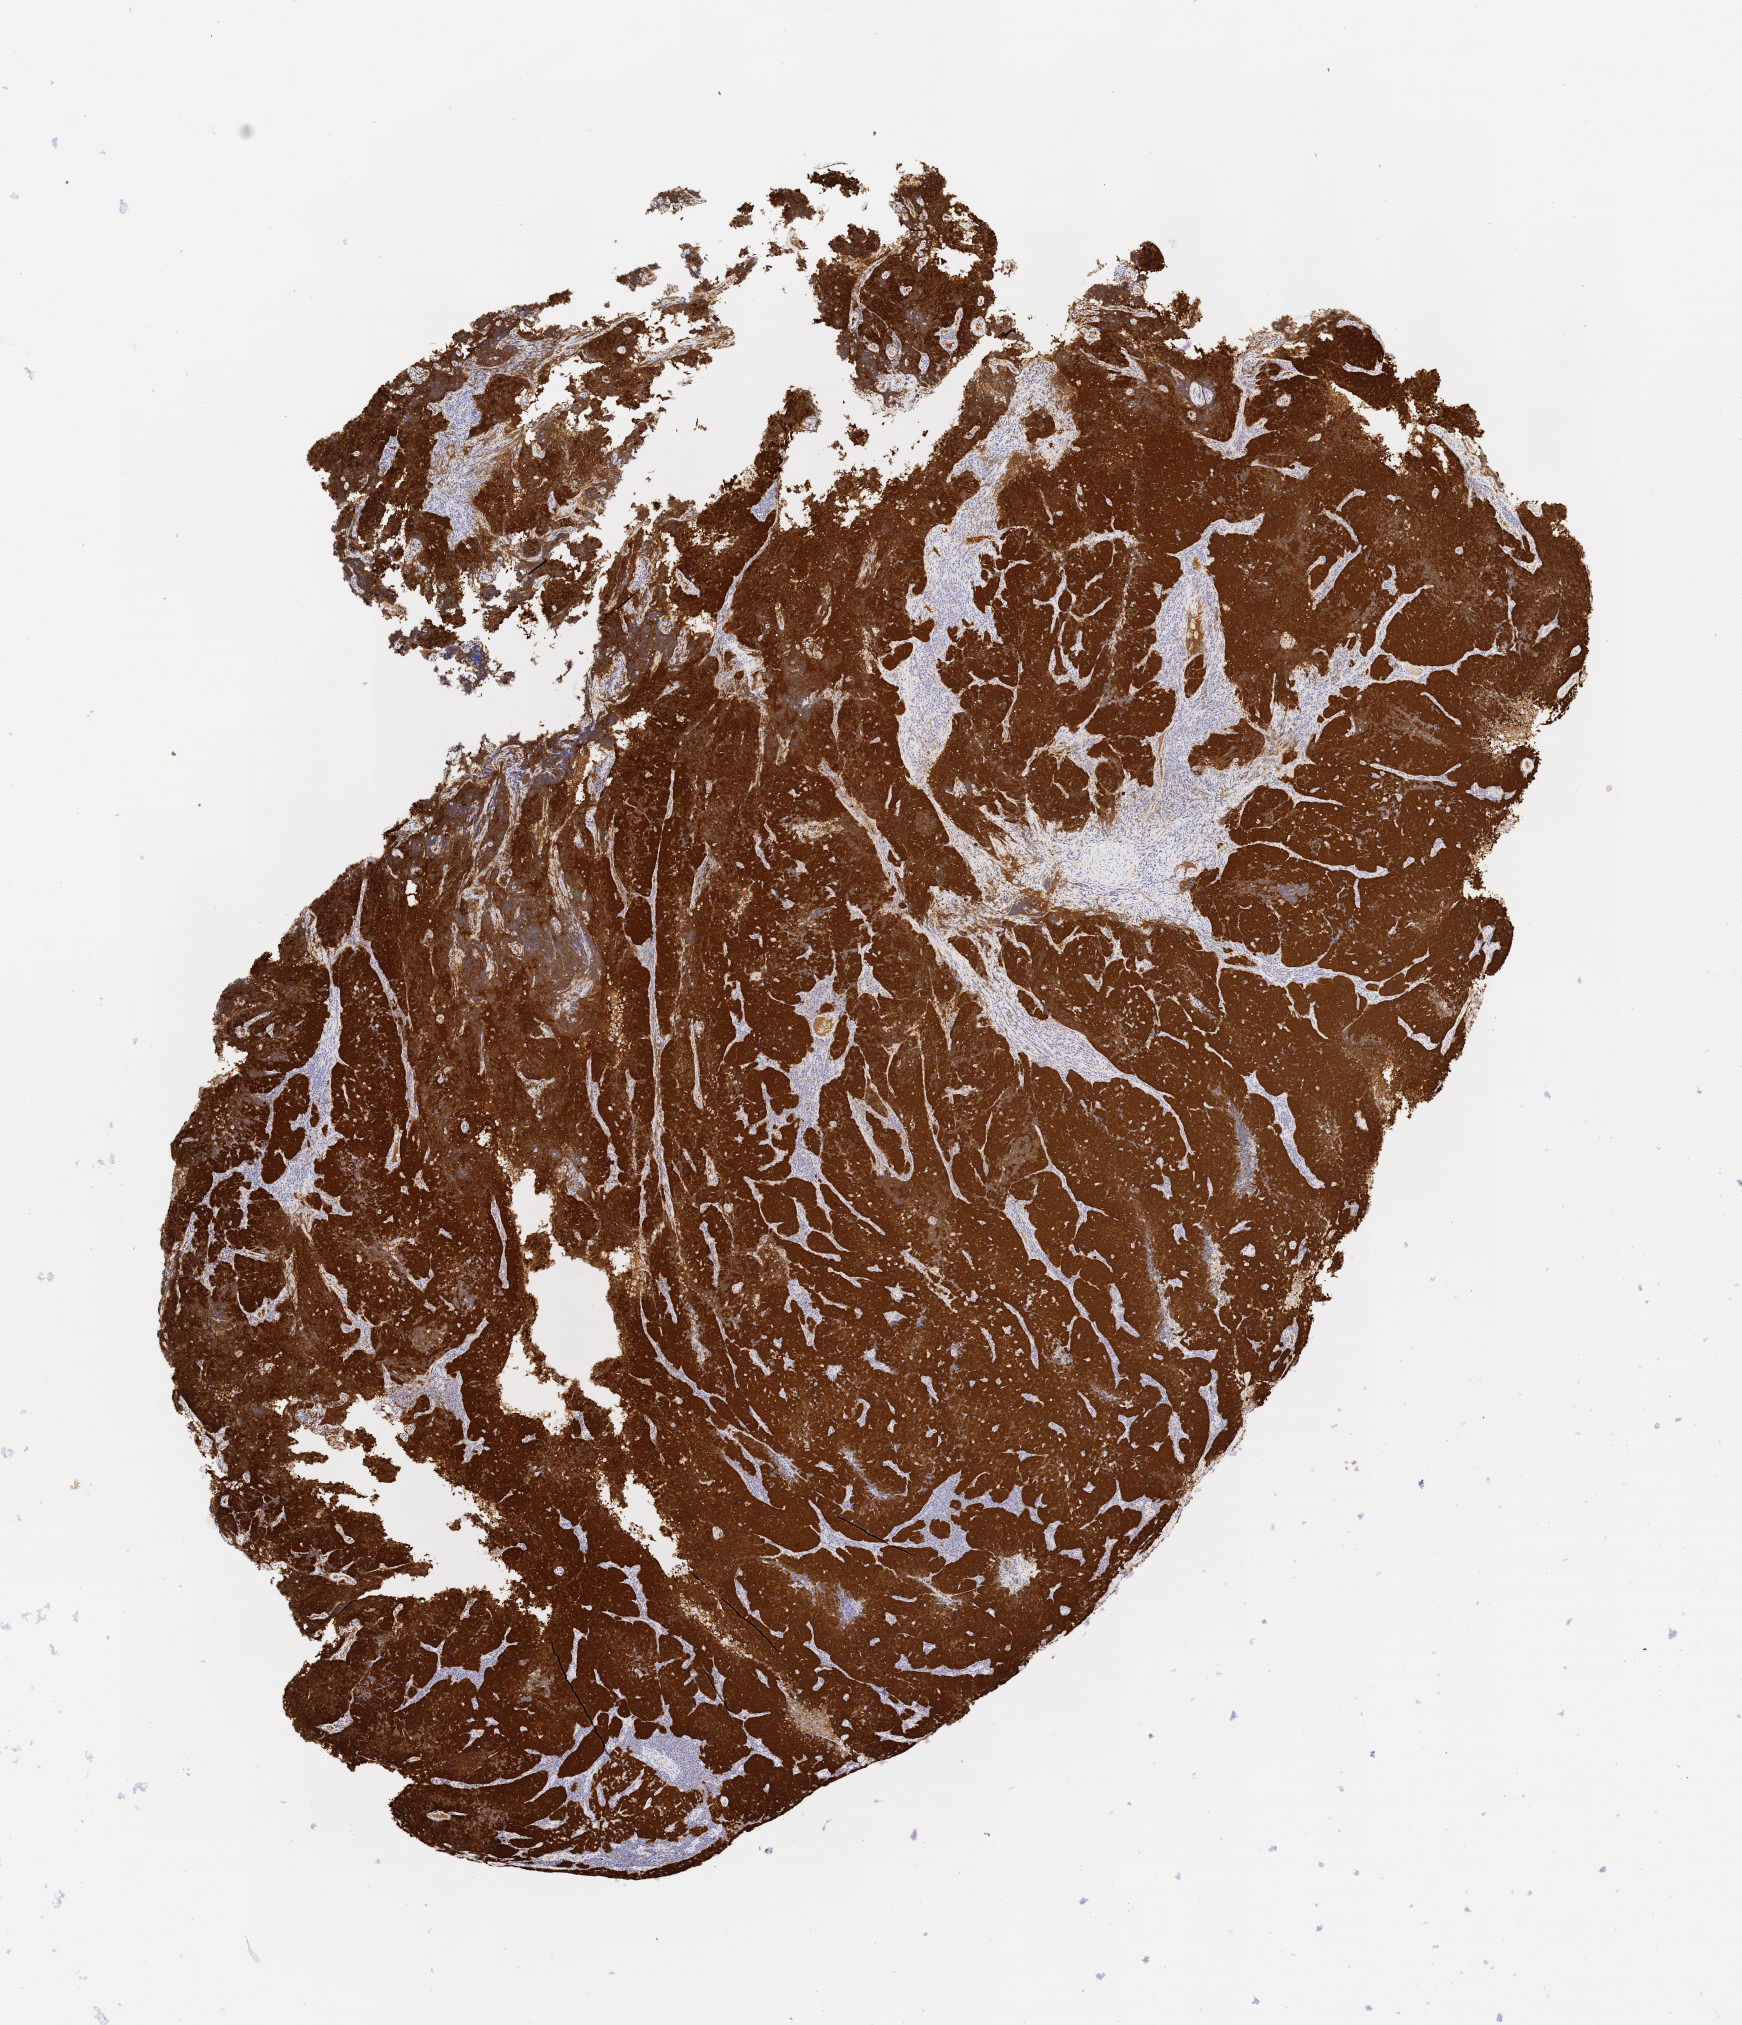
Whole-slide image, immunohistochemical stain for p16 (p16INK4a), whole scanned area (about 7.0 x 8.2 mm) shown as a low-resolution overview; tumor tissue; anatomic site: cervix. Patient: female, aged 40.
• diagnosis: Small cell carcinoma, NOS